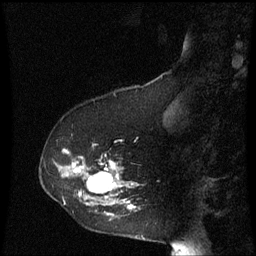
Breast MRI (dynamic contrast-enhanced), one sagittal slice; position 19 of 60 along the scan axis; dynamic contrast-enhanced series, image 2 of 3 at this slice position (ordered by acquisition); 1.5 T; TE 4.2 ms, TR 8.9 ms; 2 mm slice thickness; 256 × 256 image matrix. Patient: female, 53 years. From the clinical record (not read from this slice): setting: breast cancer imaged before/during neoadjuvant chemotherapy; receptor status: HR-positive, HER2-negative.
Annotated regions visible in this slice (semi-automatically segmented with operator editing):
- analysis volume of interest (the breast-tissue region the enhancement analysis was run in; not a lesion): box from (x=40, y=144) to (x=139, y=221) px
- tumour enhancement mask (voxels above the 70 % enhancement threshold inside the analysis volume of interest): (x=74, y=162)–(x=133, y=217)